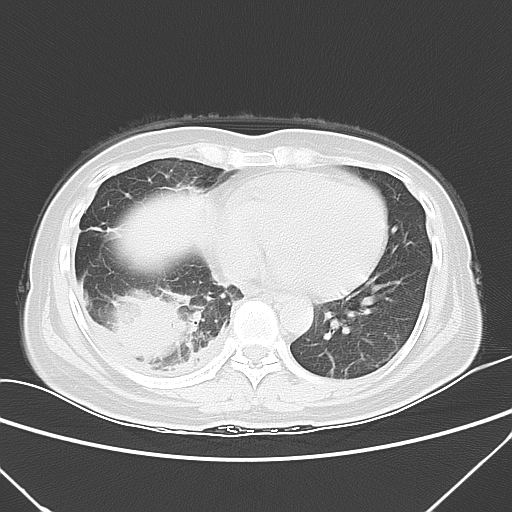
Chest CT, one axial slice; slice 16 of 53 in the series (ordered by position); lung window (W 1500 / L -600 HU); 5 mm slice thickness; 512 × 512 image matrix. Patient: female, 42 years. Case-level facts recorded for this patient, not image findings: clinical TNM (as recorded): T3 N0 M1c.
Outlined on this slice (bounding box drawn by a radiologist):
- lung tumour (recorded histology: adenocarcinoma): bounding box [x1, y1, x2, y2] px = [107, 286, 202, 368]